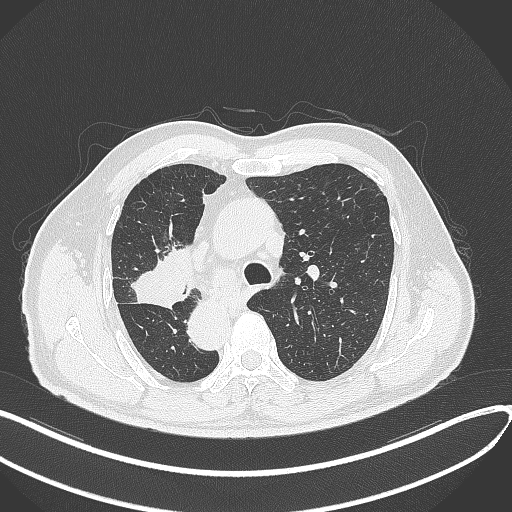
Chest CT, one axial slice. Slice 212 of 300 in the series (ordered by position). Reconstruction kernel B70f. Lung window (W 1500 / L -600 HU). 1 mm slice thickness. 512 × 512 image matrix. Male patient, age 67 years. From the clinical record (not read from this slice): clinical TNM (as recorded): T2a N0 M0.
Annotated regions visible in this slice (rectangle marked by the reading radiologist):
- lung tumour (recorded histology: squamous cell carcinoma): bounding box <132,257,190,311> (left, top, right, bottom; pixels)